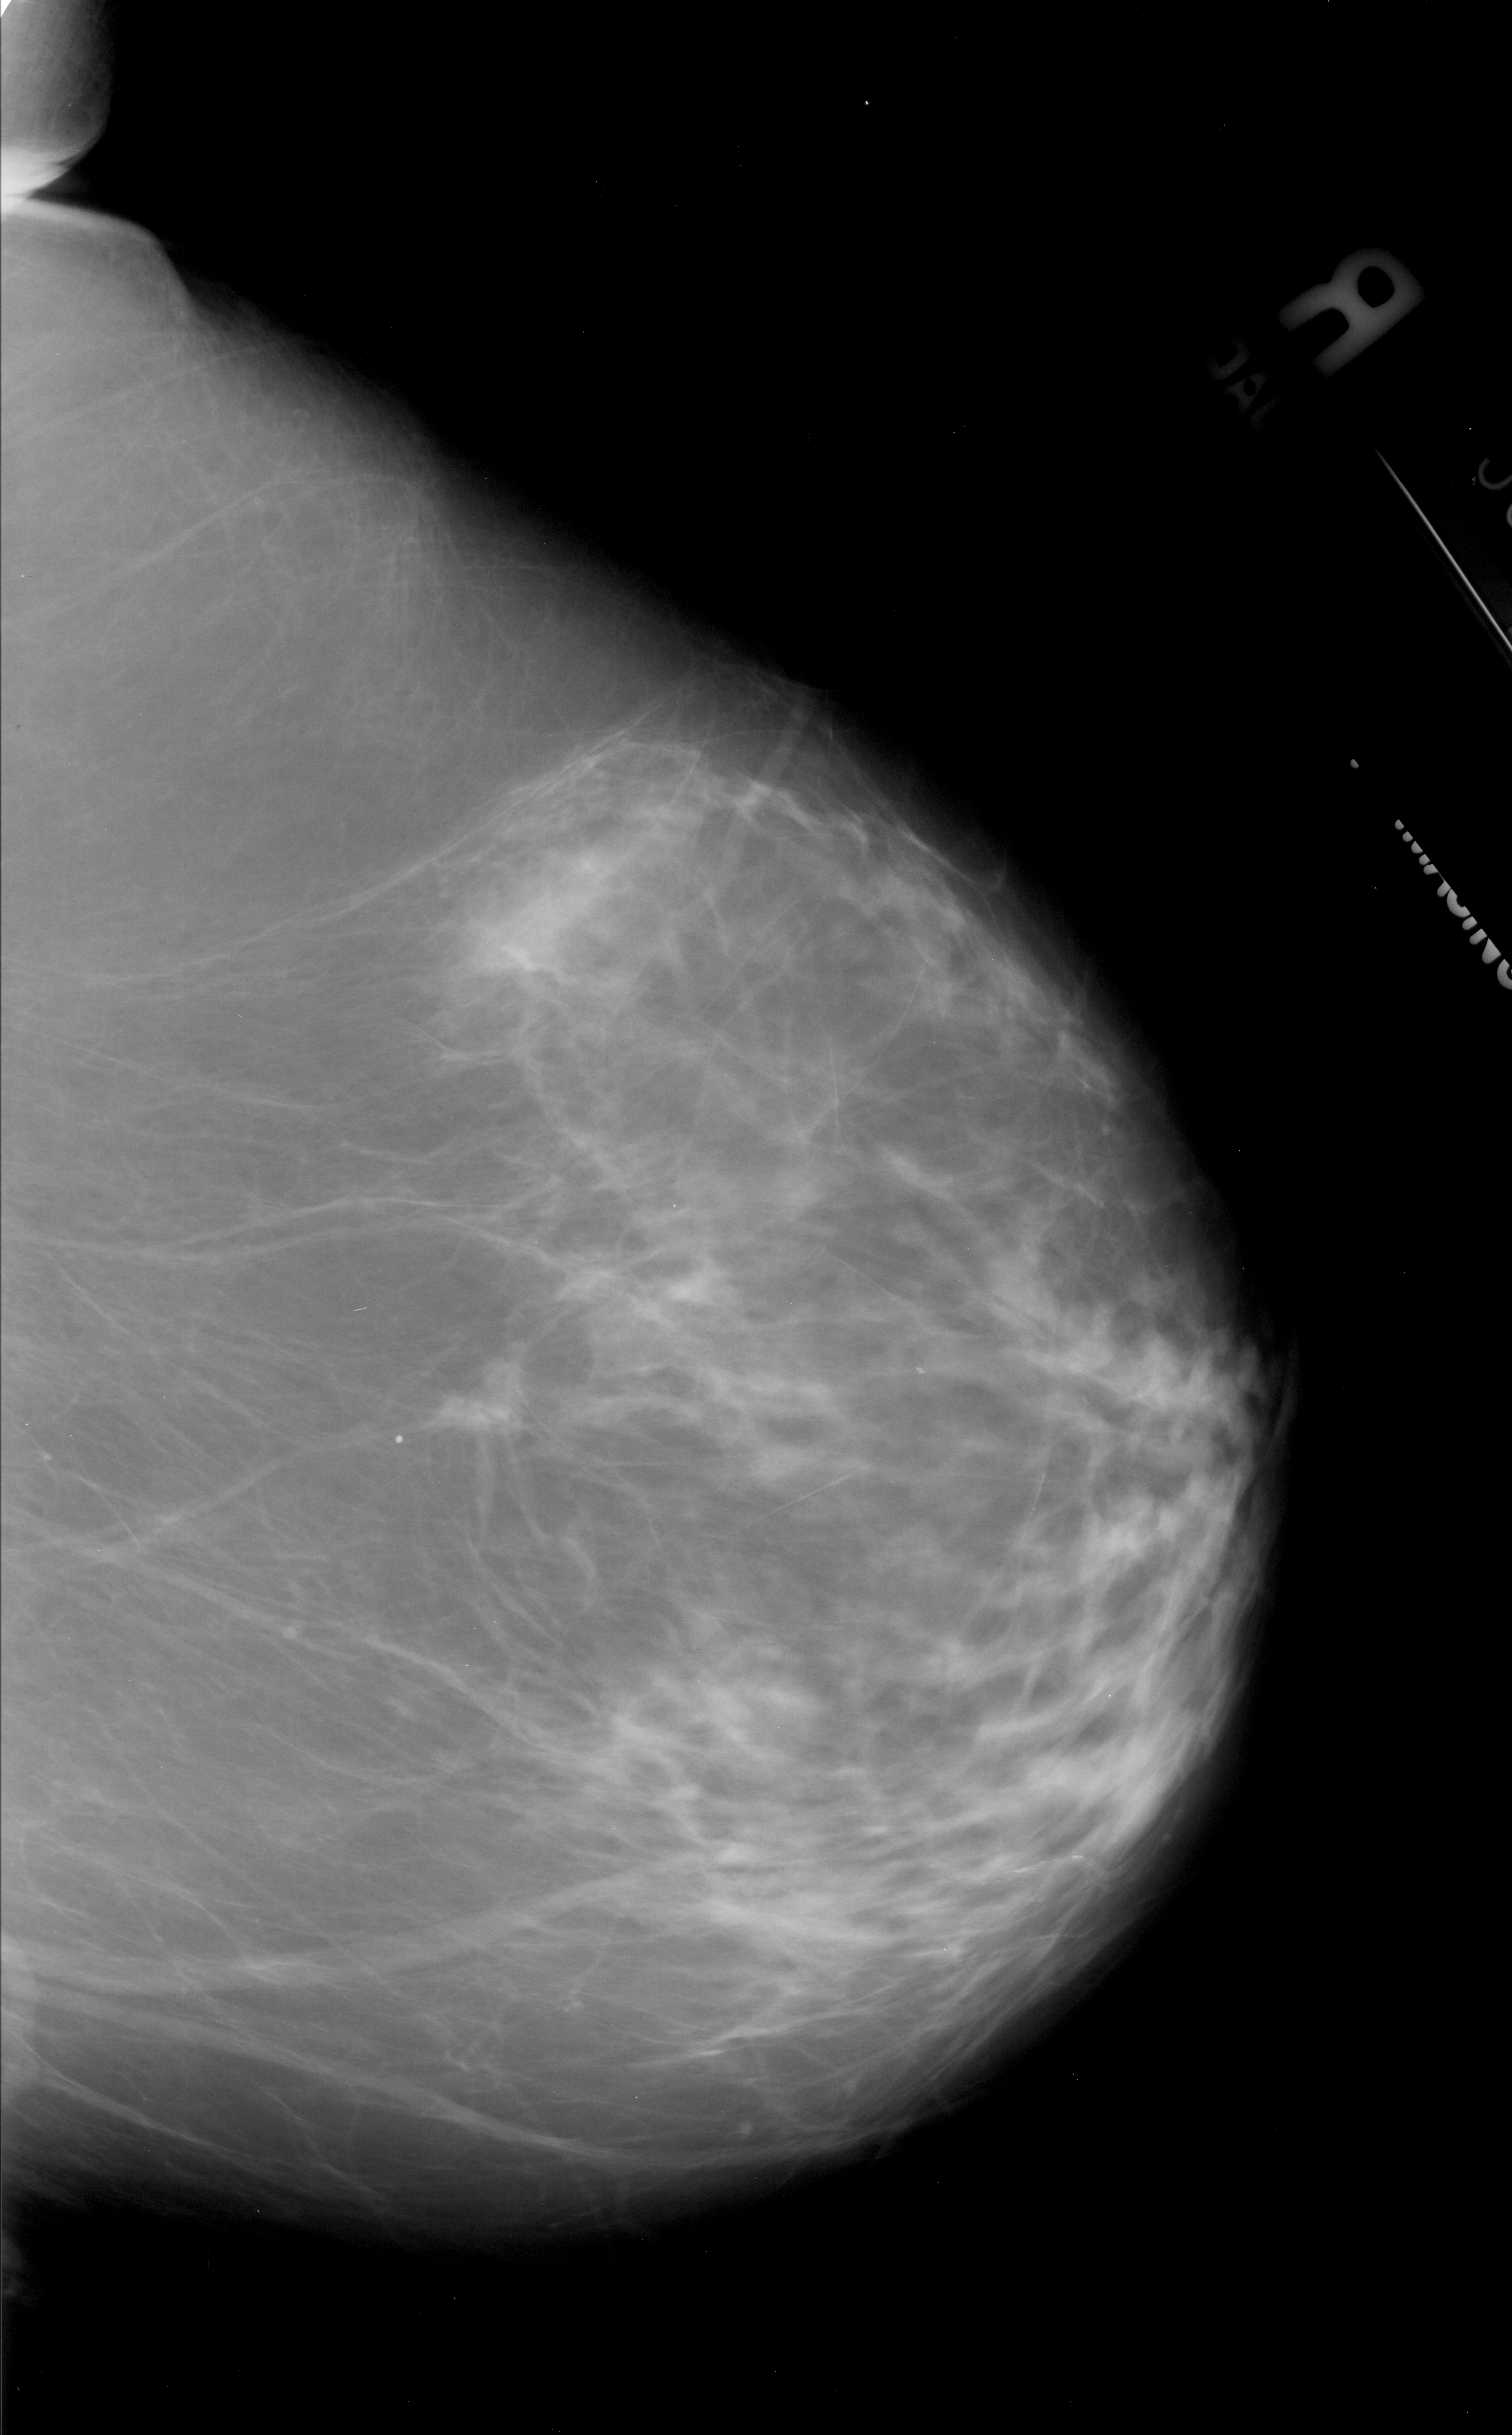
Digitized screen-film mammogram; right breast; craniocaudal (CC) view; BI-RADS breast density category 2 (scale 1–4); 1512 × 2435 image matrix.
Expert-marked regions of interest on this film, with their recorded descriptors:
- mass, shape irregular, margins spiculated; BI-RADS assessment category 5; pathology result (as recorded, not read from the image): malignant: bounding box (x1, y1, x2, y2) in pixels: (418, 1341, 539, 1477)